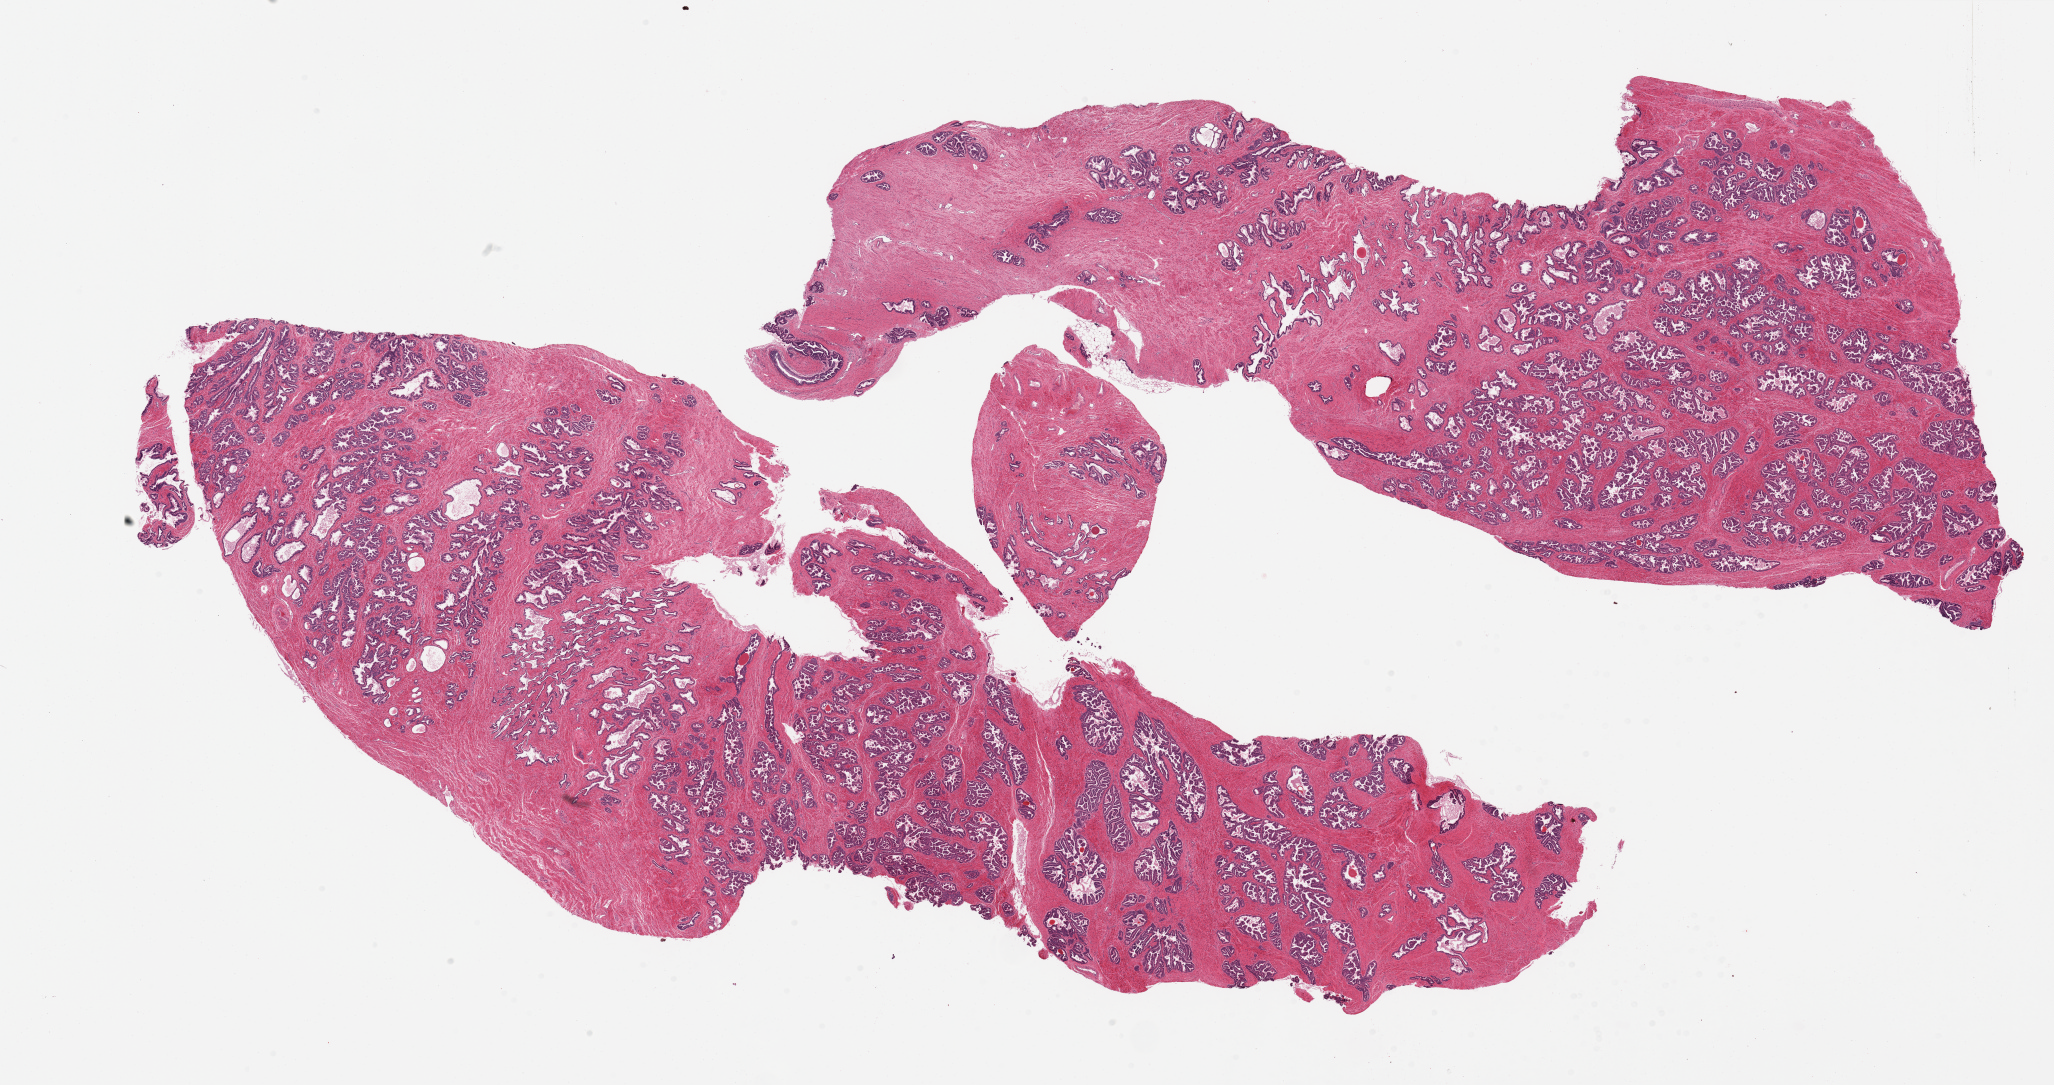
Whole-slide image, hematoxylin and eosin (H&E) stain, shown as a low-resolution overview of the whole scanned area (about 32.5 x 17.2 mm, slide scanned at 20x). PAXgene-fixed paraffin-embedded (PFPE) section. Section of prostate (target tissue). Tissue donor sample. Donor sex: male.
Pathologist's review note for this sample: 2 pieces; well preserved.